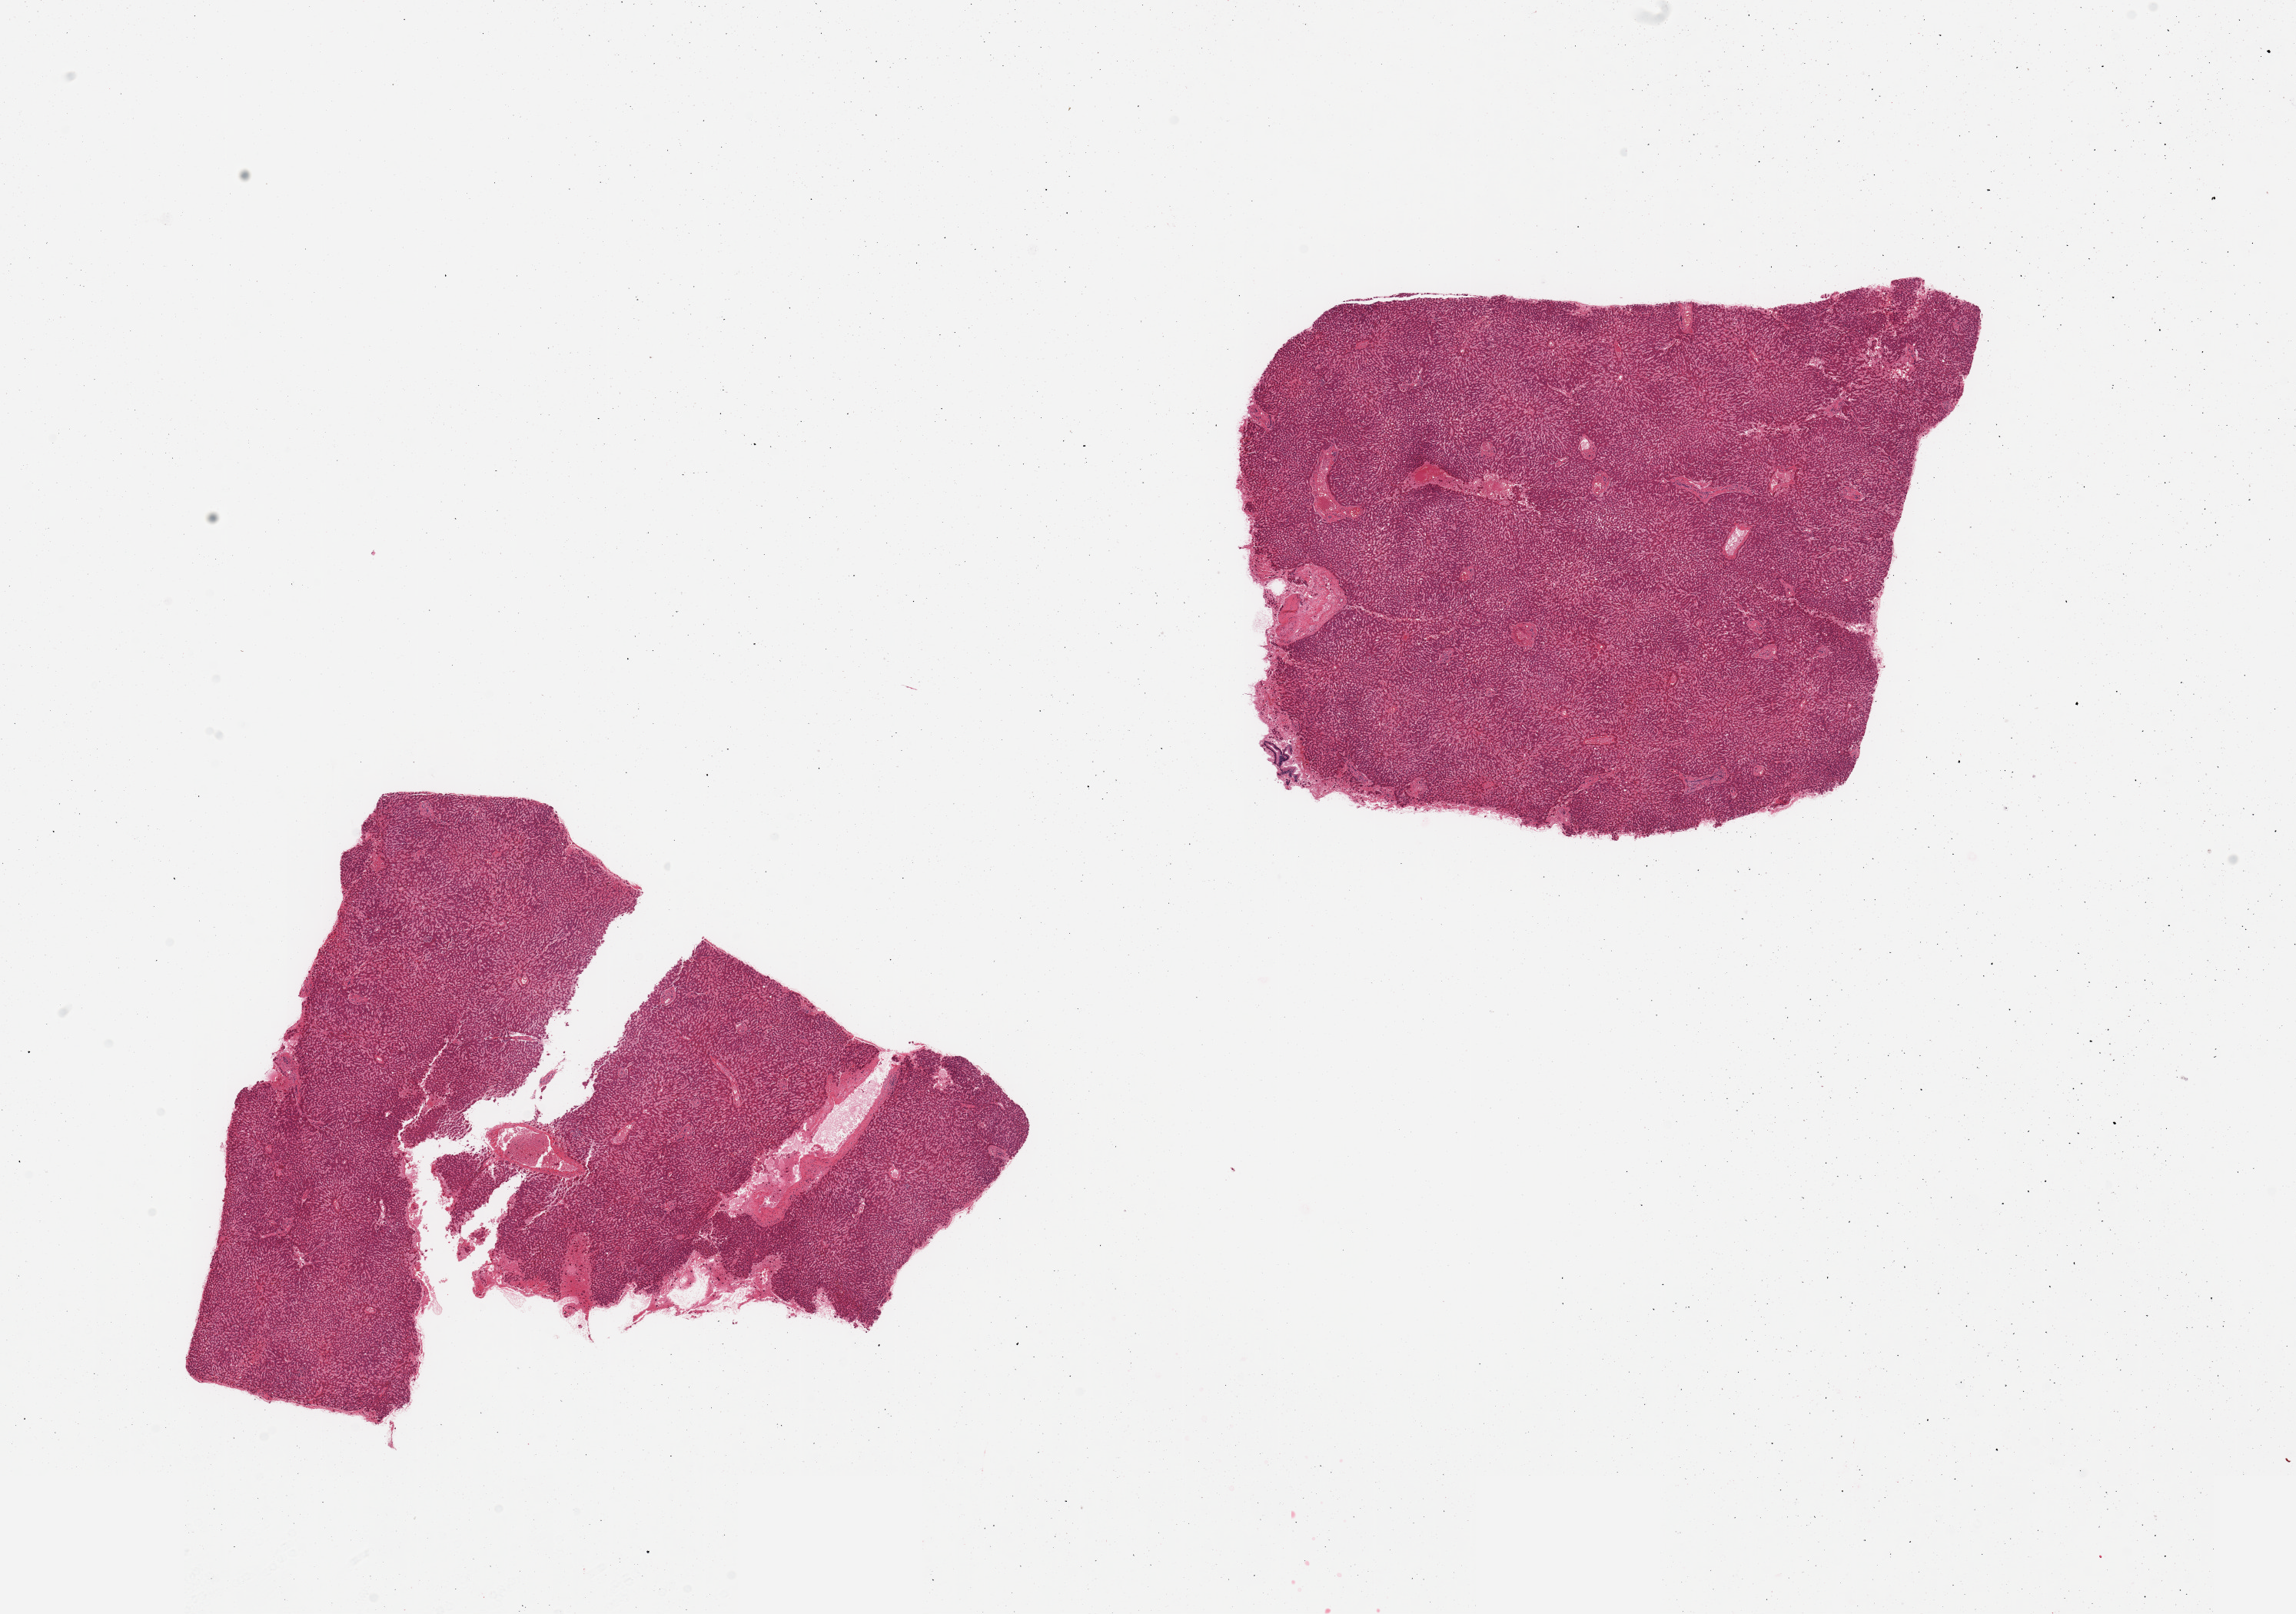
Digitized haematoxylin and eosin-stained section — whole scanned area (about 23.6 x 16.6 mm, from a 20x scan) shown as a low-resolution overview; PAXgene-fixed, paraffin-embedded tissue; target tissue: liver; donor tissue sample. Female donor.
- pathologist's review note for this sample: 2 pieces; minimal fat